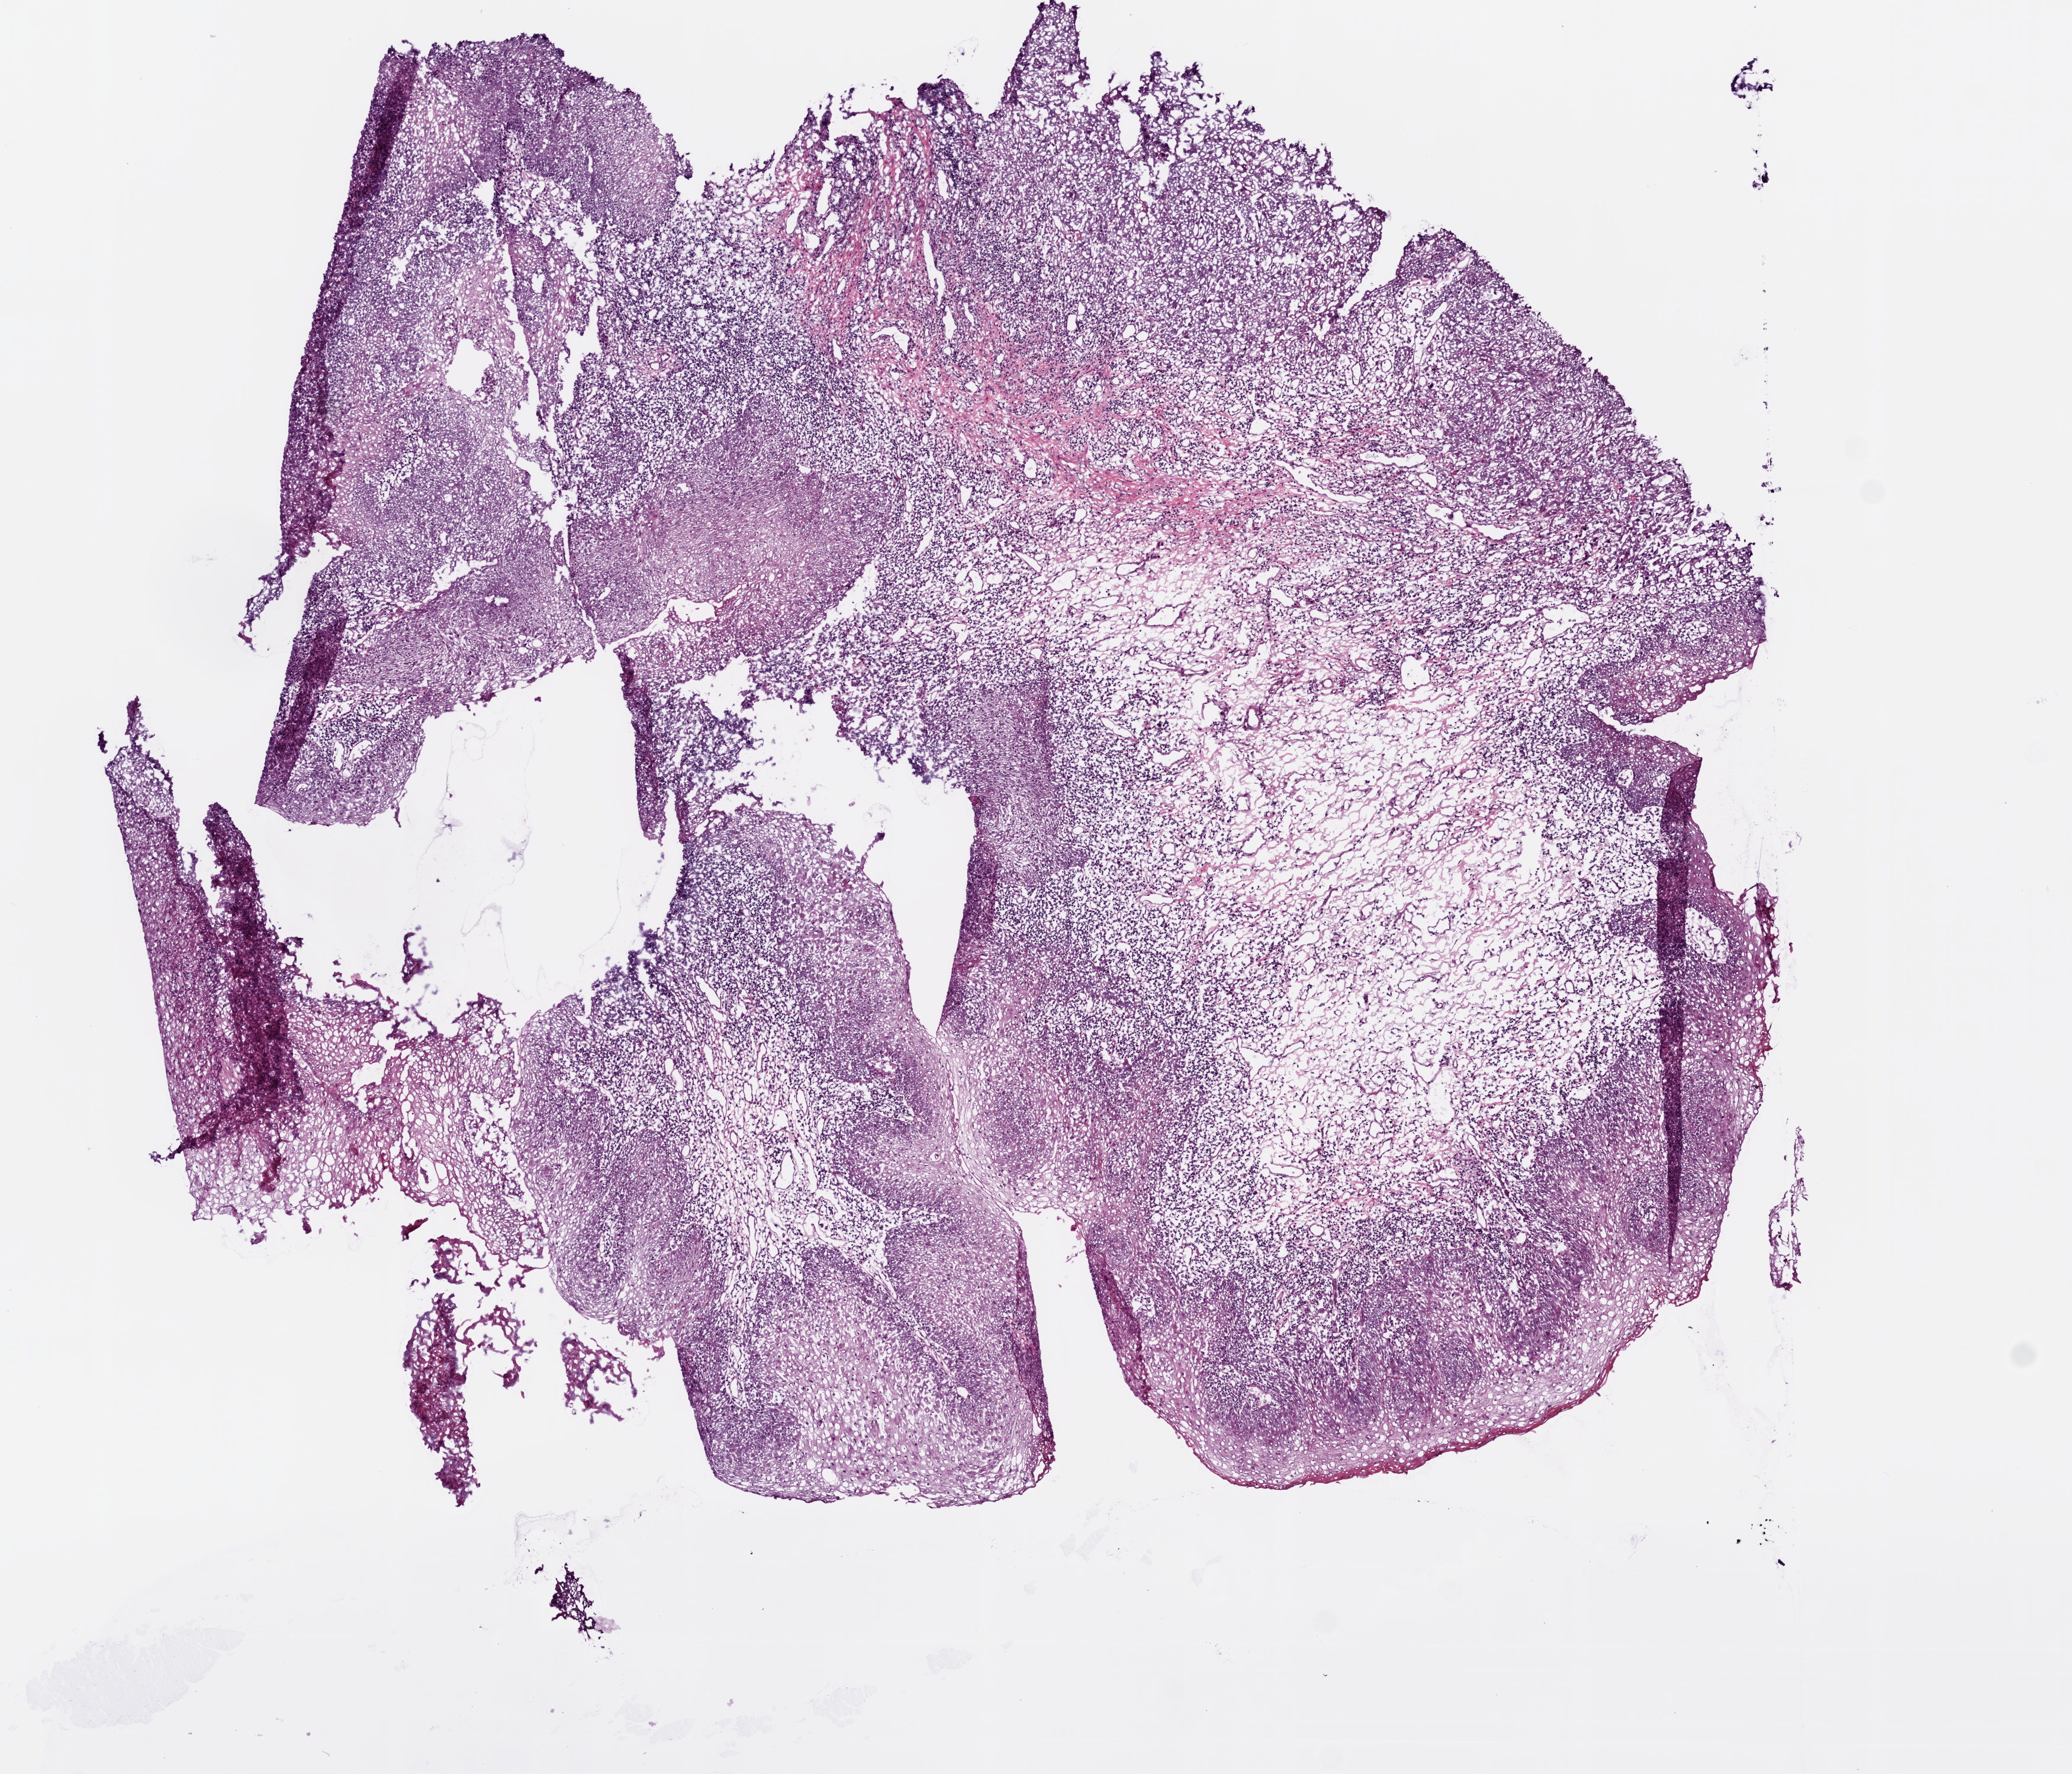
H&E whole-slide image — whole scanned area (about 7.0 x 6.0 mm) shown as a low-resolution overview. Frozen section from the bottom of the tissue portion. Sample: primary tumour, head and neck. Female, age 58 years at initial diagnosis. Histologic grade: G3 (poorly differentiated). Pathologist review of this section (percent, as recorded): tumour cells 65%, tumour nuclei 65%, normal cells 0%, stromal cells 35%, necrosis 0%.
TNM: T2 N0. AJCC pathologic stage: II (7th edition). Lymph nodes positive (case pathology): 0 of 81 examined. Diagnosis: Squamous cell carcinoma, NOS.